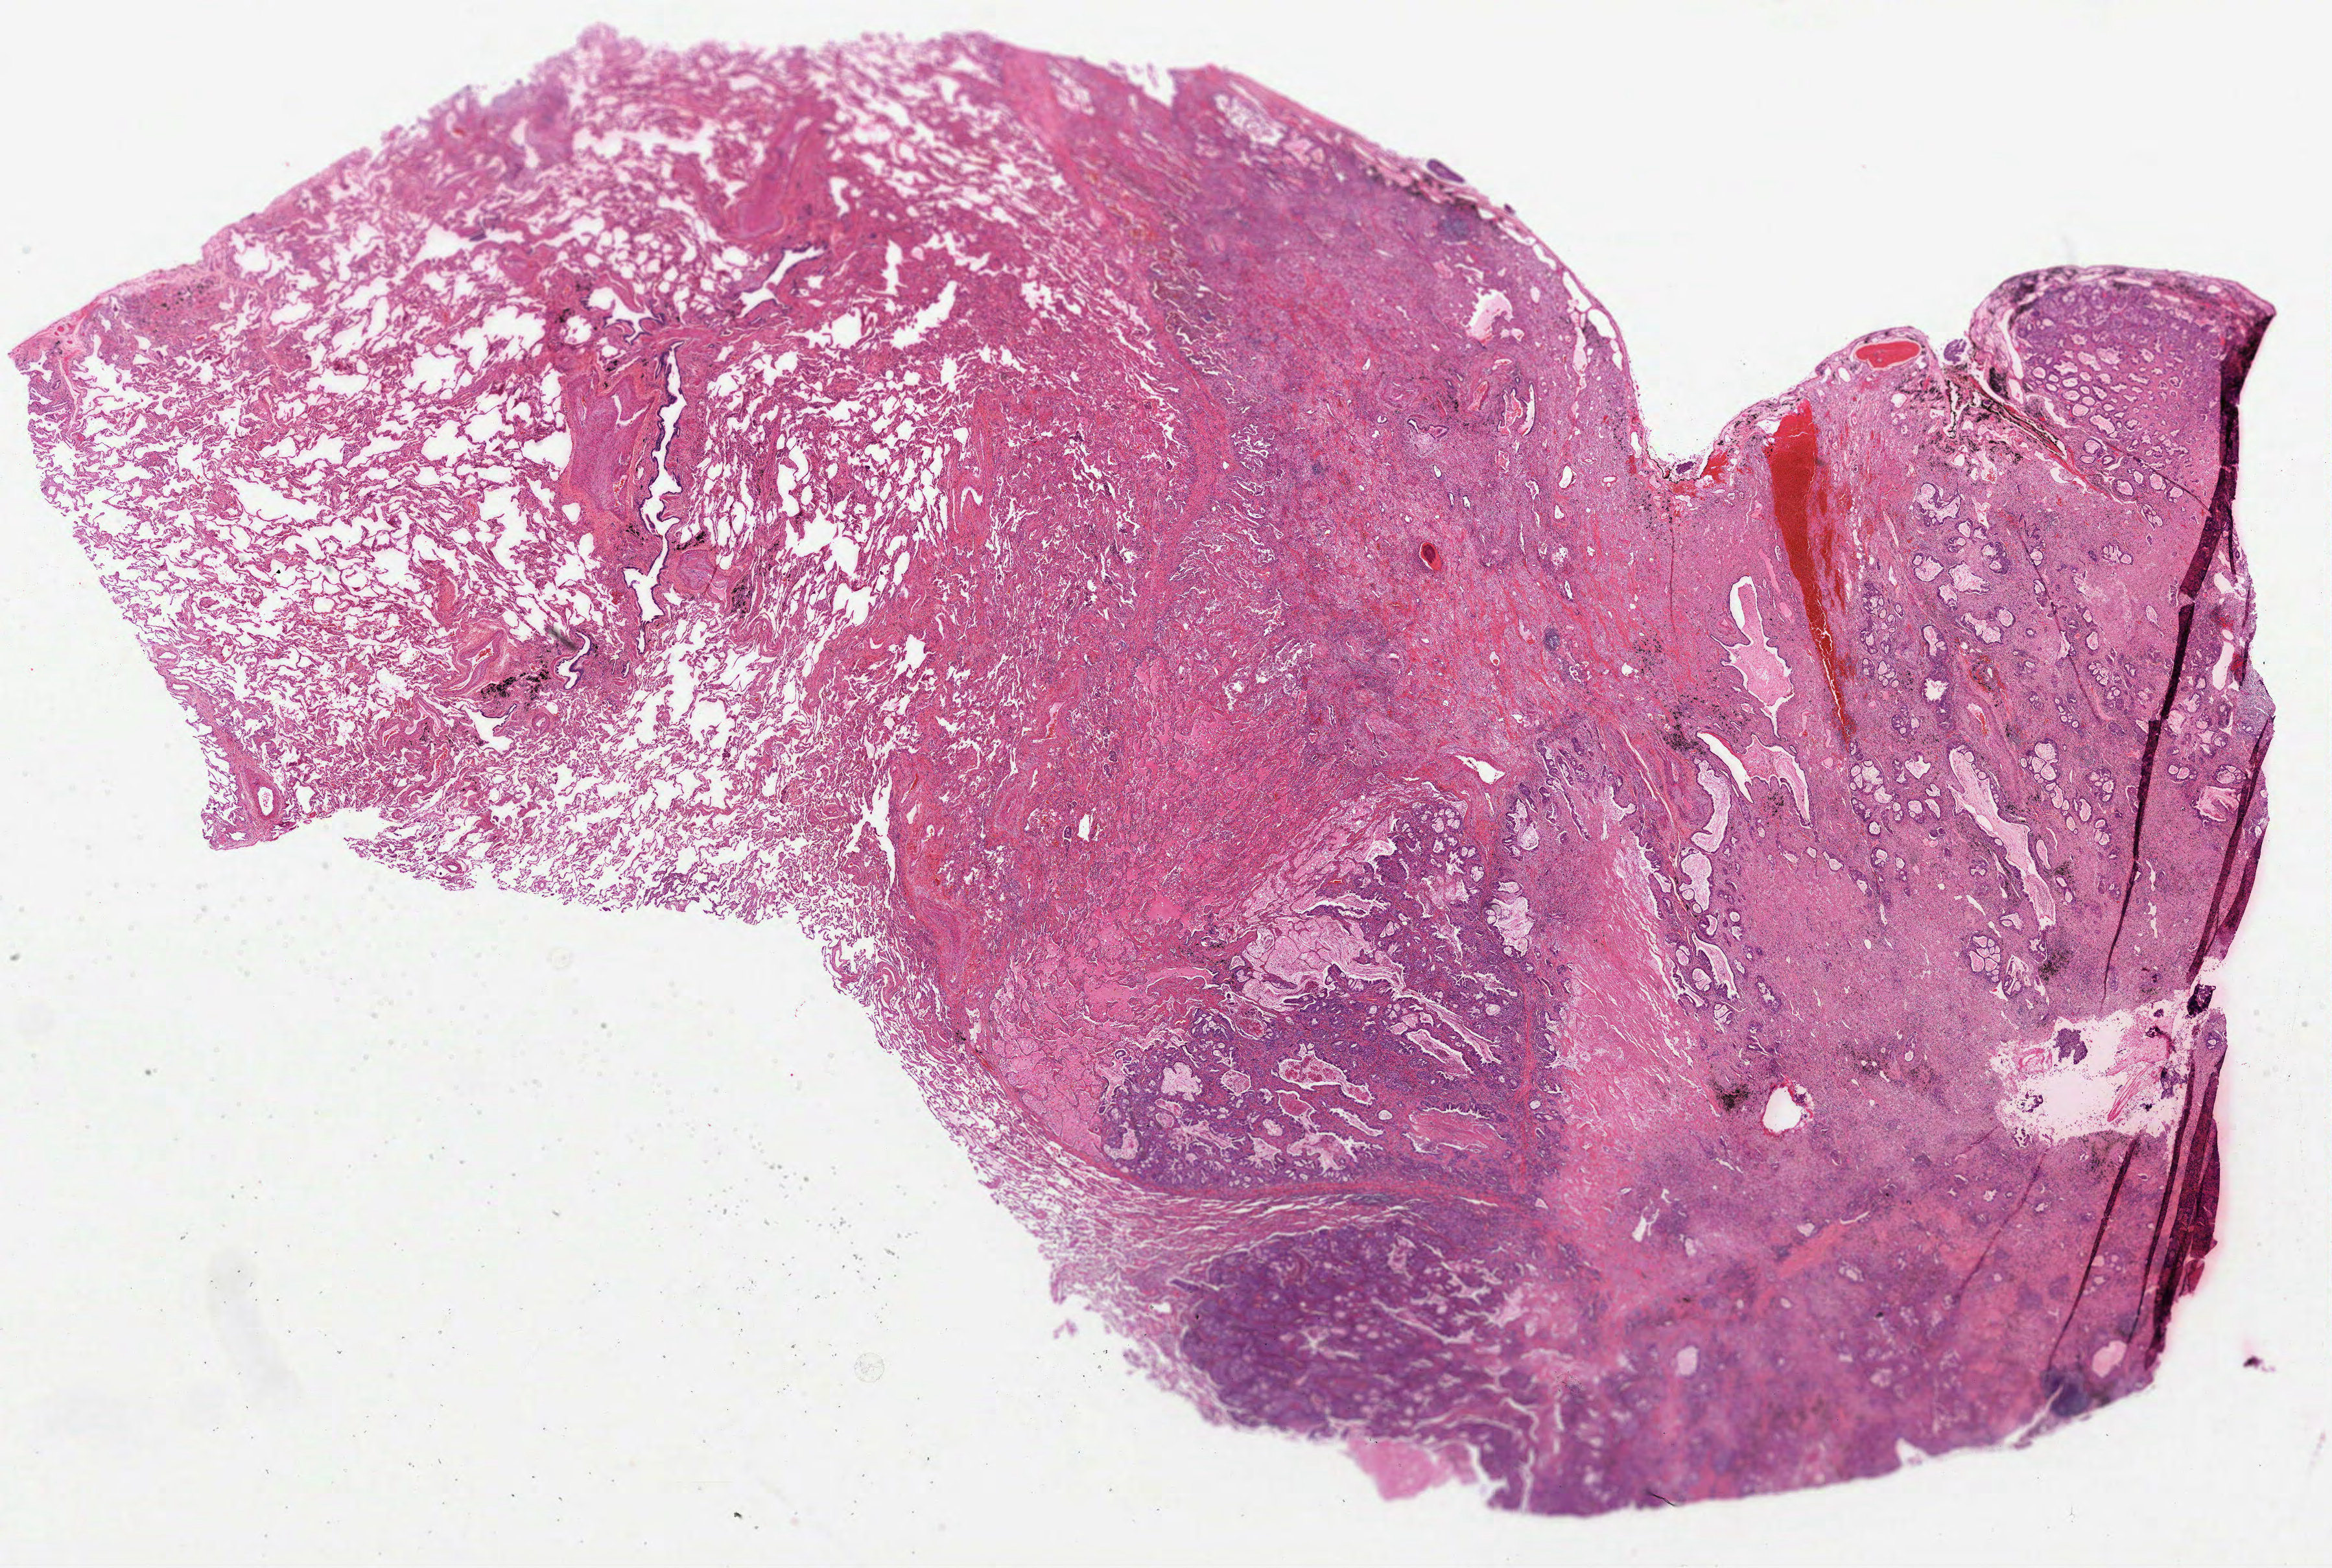
Digitized H&E-stained tissue section (whole slide) — whole scanned area (about 29.0 x 19.5 mm, slide scanned at 40x) shown as a low-resolution overview. FFPE section. Primary tumour sample from the lung. Patient: male, age at initial diagnosis 77 years.
Histologic diagnosis: Adenocarcinoma, NOS (upper lobe, lung).